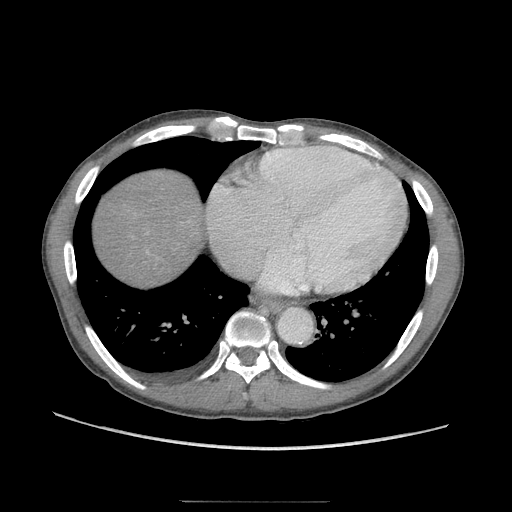
Contrast-enhanced abdominal CT (liver protocol), one axial slice. Slice 96 of 103 in the series (ordered by position). Reconstruction kernel STANDARD. Soft-tissue window (W 400 / L 40 HU). 2.5 mm slice thickness. 512 × 512 image matrix, field of view 380 × 380 mm. From the clinical record (not read from this slice): diagnosis: hepatocellular carcinoma (patient treated with transarterial chemoembolisation; whether this scan precedes or follows treatment is not stated here); TNM stage (as recorded): Stage-IIIA; Child-Pugh class: A; tumour differentiation: moderately differentiated; tumour nodularity: multinodular.
Annotated regions visible in this slice (semi-automatic segmentation, software-assisted and operator-edited):
- abdominal aorta: box from (x=278, y=307) to (x=311, y=343) px
- liver parenchyma outside the tumour (the mass and vessels are separate outlines, so this box may not span the whole liver): (x=96, y=172)–(x=200, y=278)